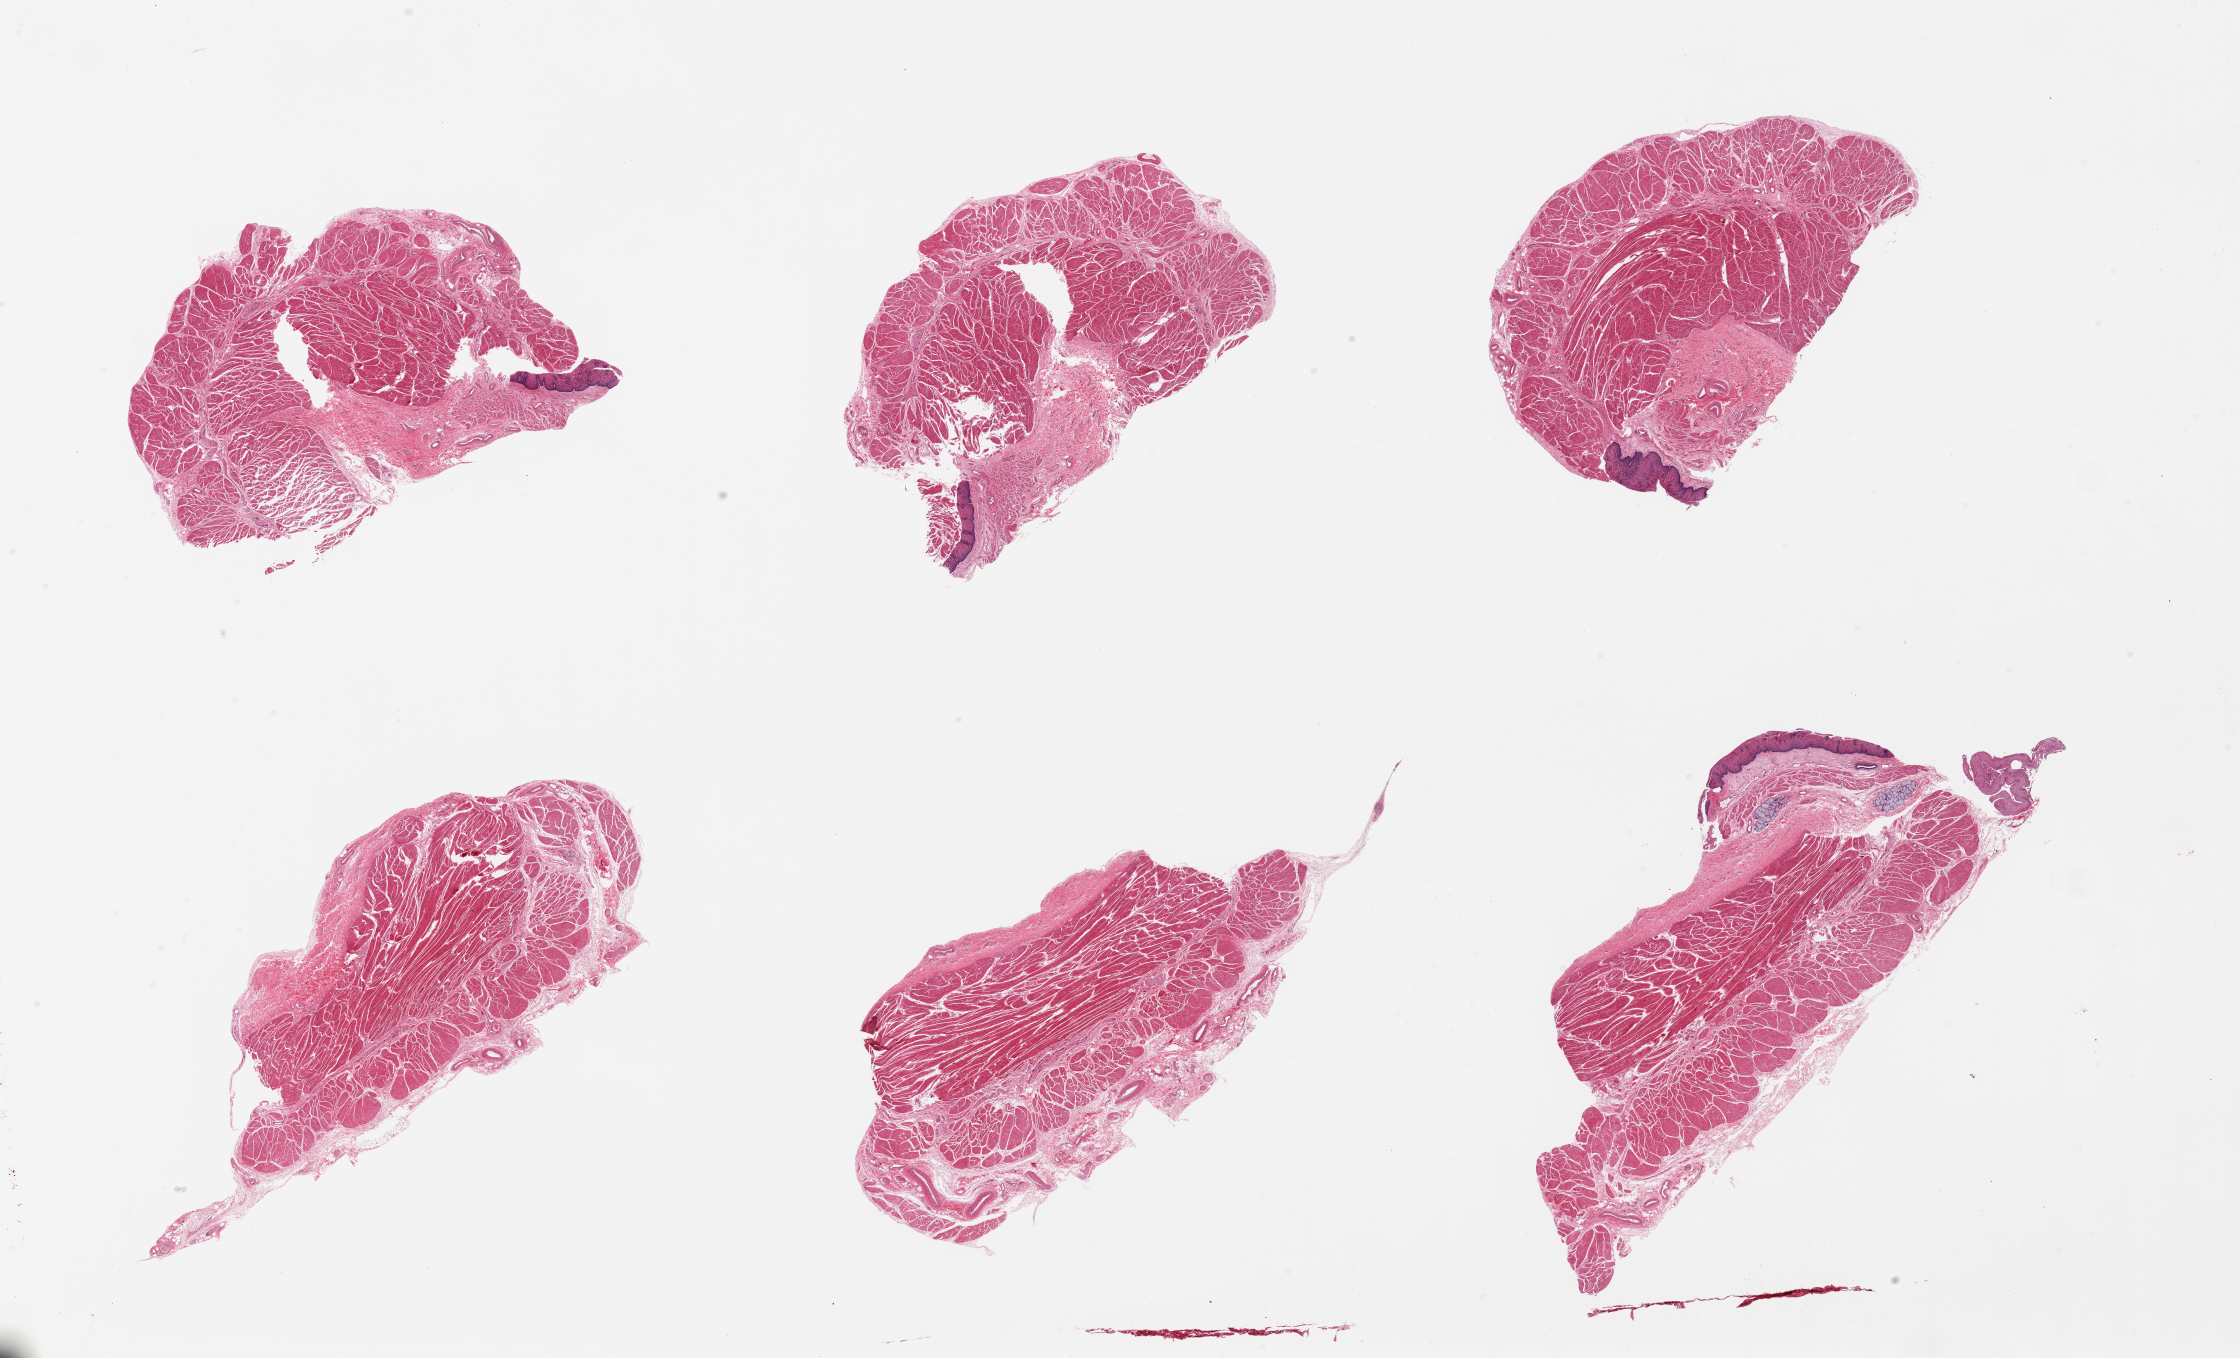
Whole-slide image, H&E stain — low-resolution overview of the scanned area, about 35.4 x 21.5 mm, PAXgene-fixed paraffin-embedded (PFPE) section, sampled site (target tissue): gastroesophageal junction, donor tissue sample.
Pathologist's review note for this sample: 6 pieces, predominantly muscularis, trace squamous mucosalr remnants present in 4.